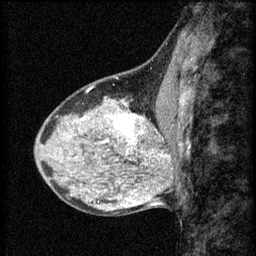
Breast MRI (dynamic contrast-enhanced), one sagittal slice. Slice 24 of 60 in the series (ordered by position). 3 images stored at this slice position (order not interpretable as contrast timing). 1.5 T. TE 4.2 ms, TR 8.2 ms. 2 mm slice thickness. 256 × 256 image matrix. Female patient, age 40 years.
Structures marked on this image (semi-automatic segmentation, software-assisted and operator-edited):
- analysis volume of interest (the breast-tissue region the enhancement analysis was run in; not a lesion): bounding box [x1, y1, x2, y2] px = [108, 108, 167, 159]
- tumour enhancement mask (voxels above the 70 % enhancement threshold inside the analysis volume of interest): [116, 114, 167, 159]